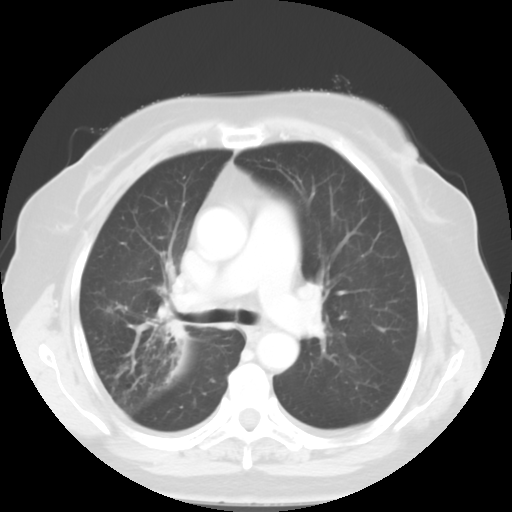
Chest CT, one axial slice. Slice 33 of 52 in the series (ordered by position). 120 kVp. Lung window (W 1500 / L -600 HU). 512 × 512 image matrix. Female patient, age 81 years. From the clinical record (not read from this slice): clinical TNM (as recorded): T4 N3 M1b.
Structures marked on this image (rectangle marked by the reading radiologist):
- lung tumour (recorded histology: adenocarcinoma): bounding box (x1, y1, x2, y2) in pixels: (154, 306, 188, 344)